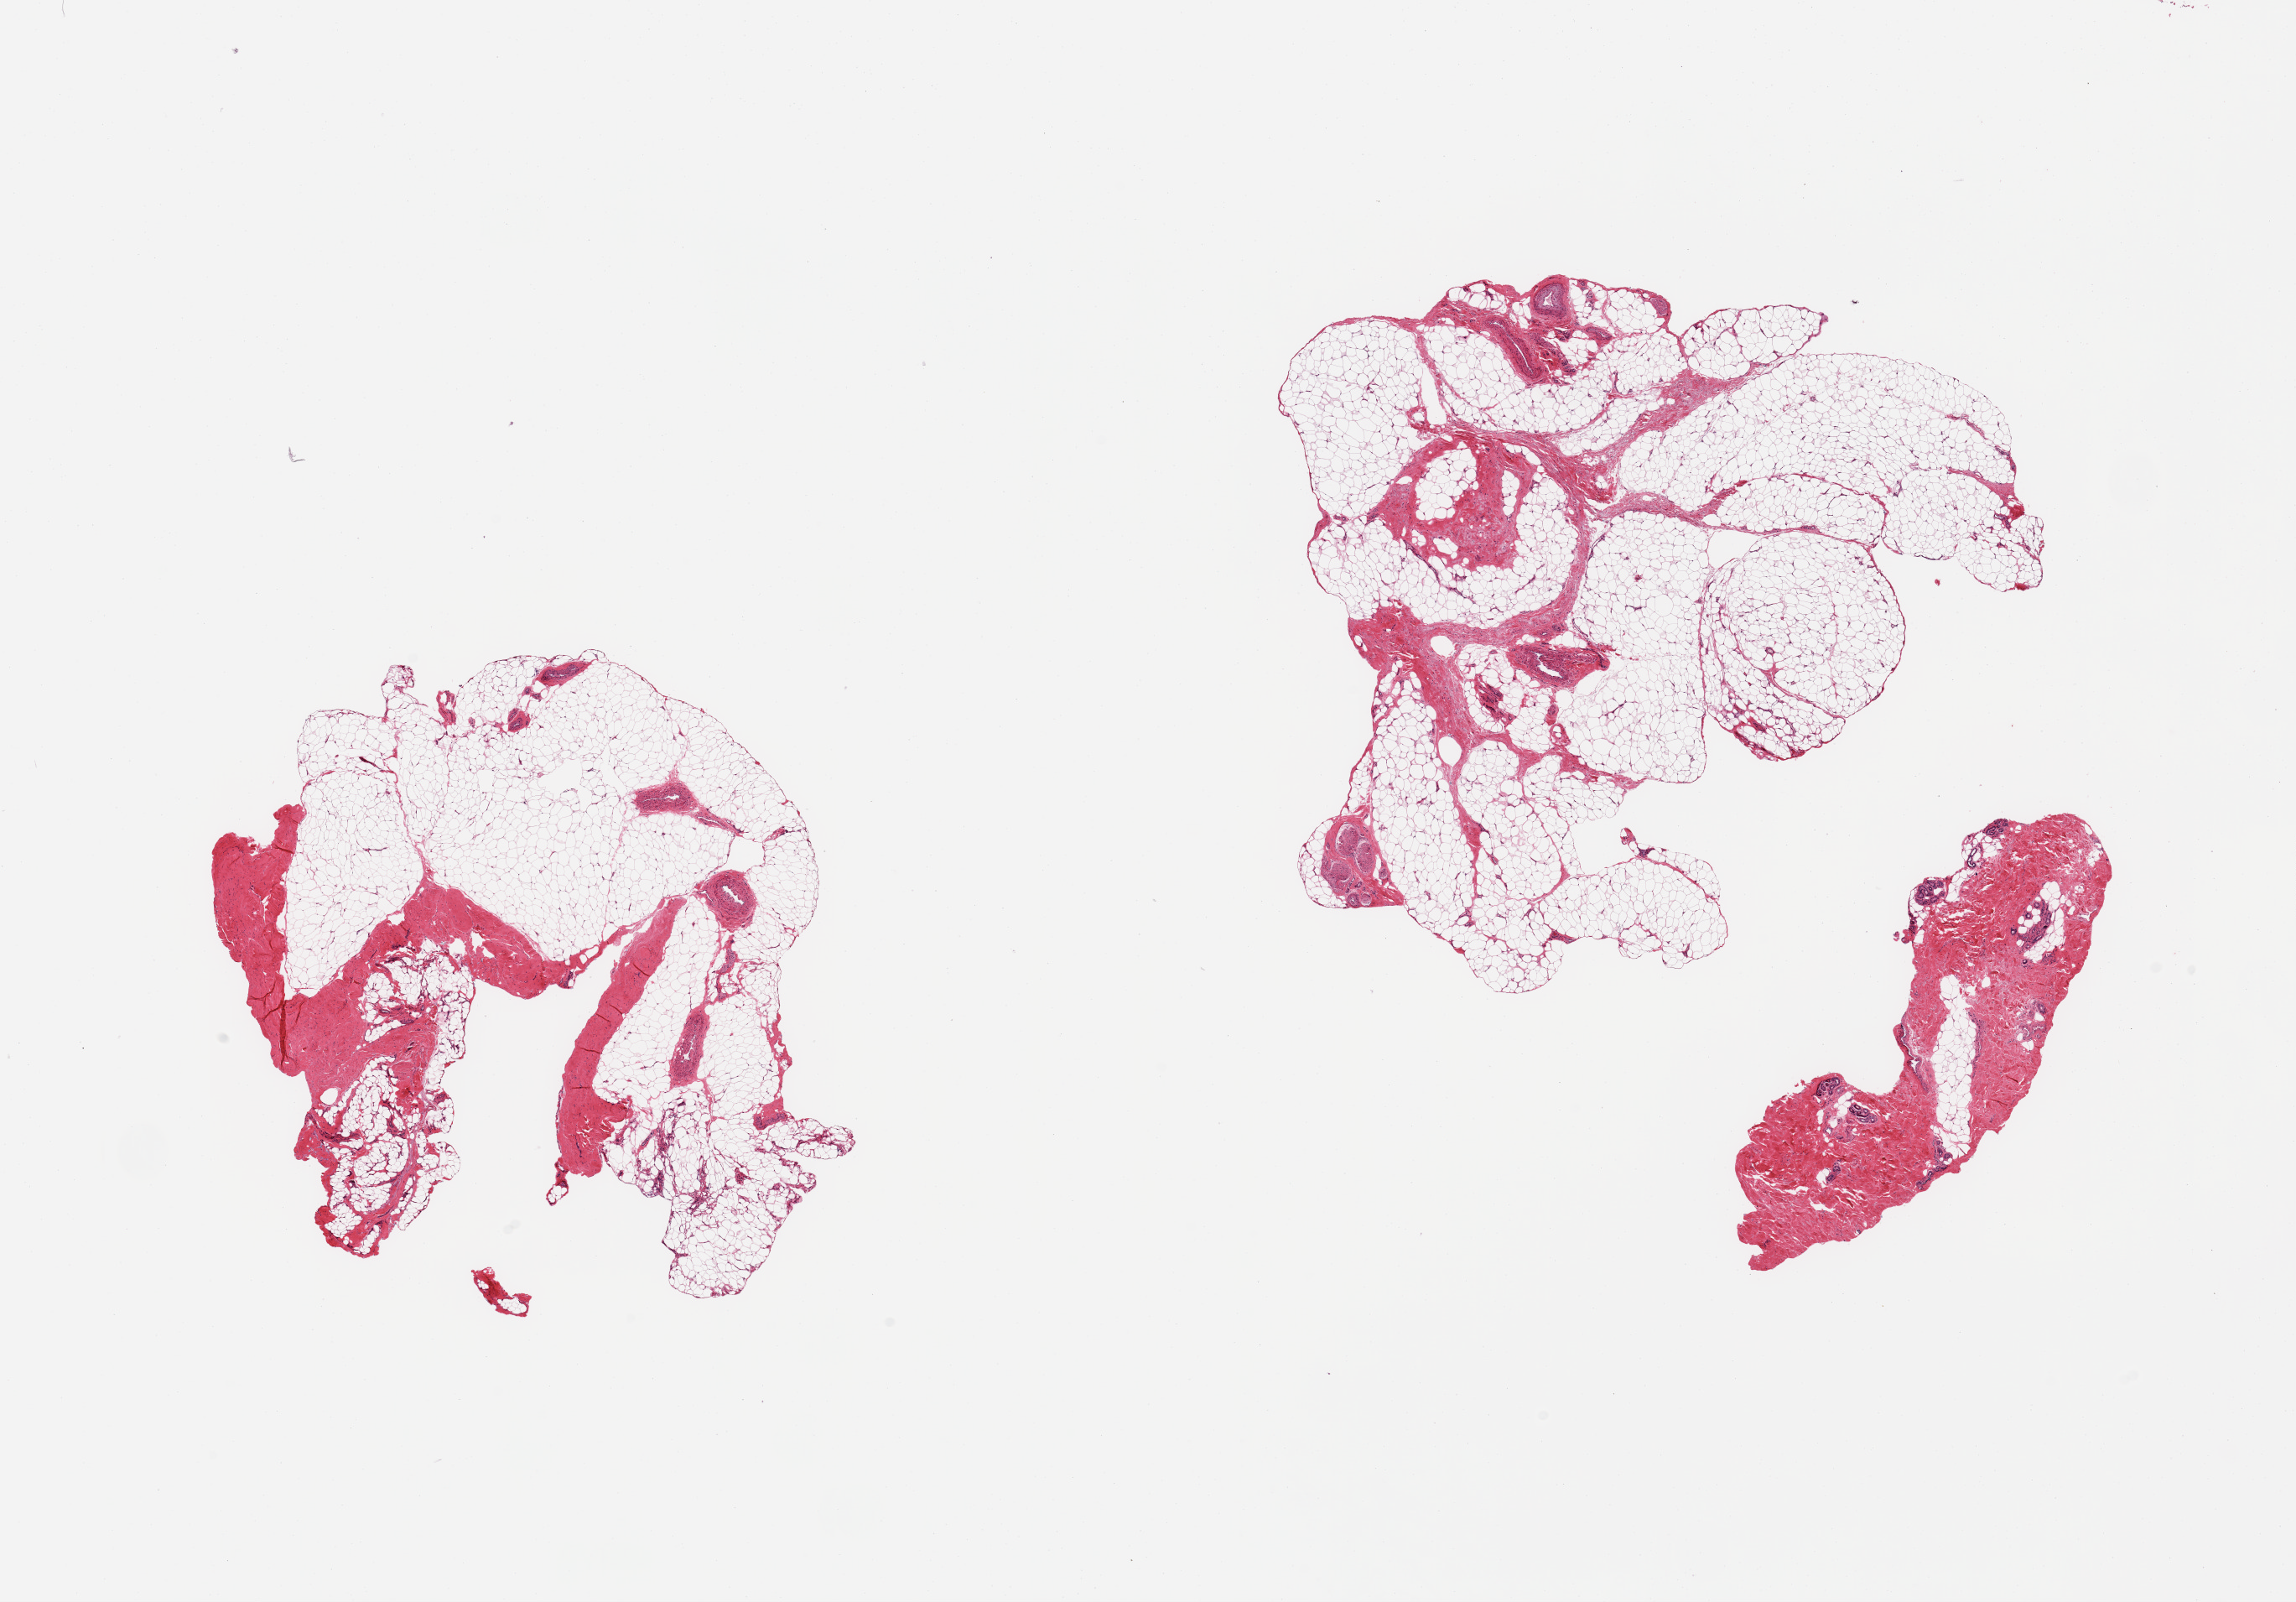
Digitized H&E-stained section — whole scanned area (about 21.7 x 15.1 mm) shown as a low-resolution overview. PAXgene-fixed, paraffin-embedded tissue. Target tissue: adipose tissue. Tissue donor sample. Donor sex: male.
Reviewer comment on this tissue sample: 3 pieces; two pieces of mature adipose tissue with ~15% fibrovascular component and nerves; the third piece represents deep dermis and fat.